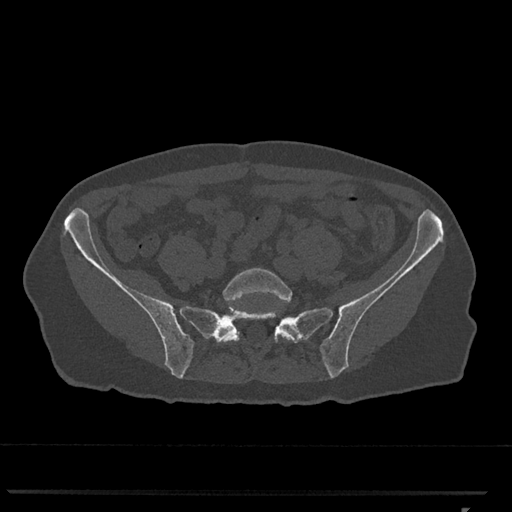
CT including the spine, one axial slice; slice 121 of 793 in the series (ordered by position); reconstruction kernel Br40s/3; bone window (W 1800 / L 400 HU); 0.5 mm slice thickness; 512 × 512 image matrix, field of view 380 × 380 mm. Patient: female, 62 years. From the clinical record (not read from this slice): primary cancer: renal.
Outlined on this slice (semi-automatic segmentation, software-assisted and operator-edited):
- L5 vertebra: bounding box <220,268,297,343> (left, top, right, bottom; pixels)